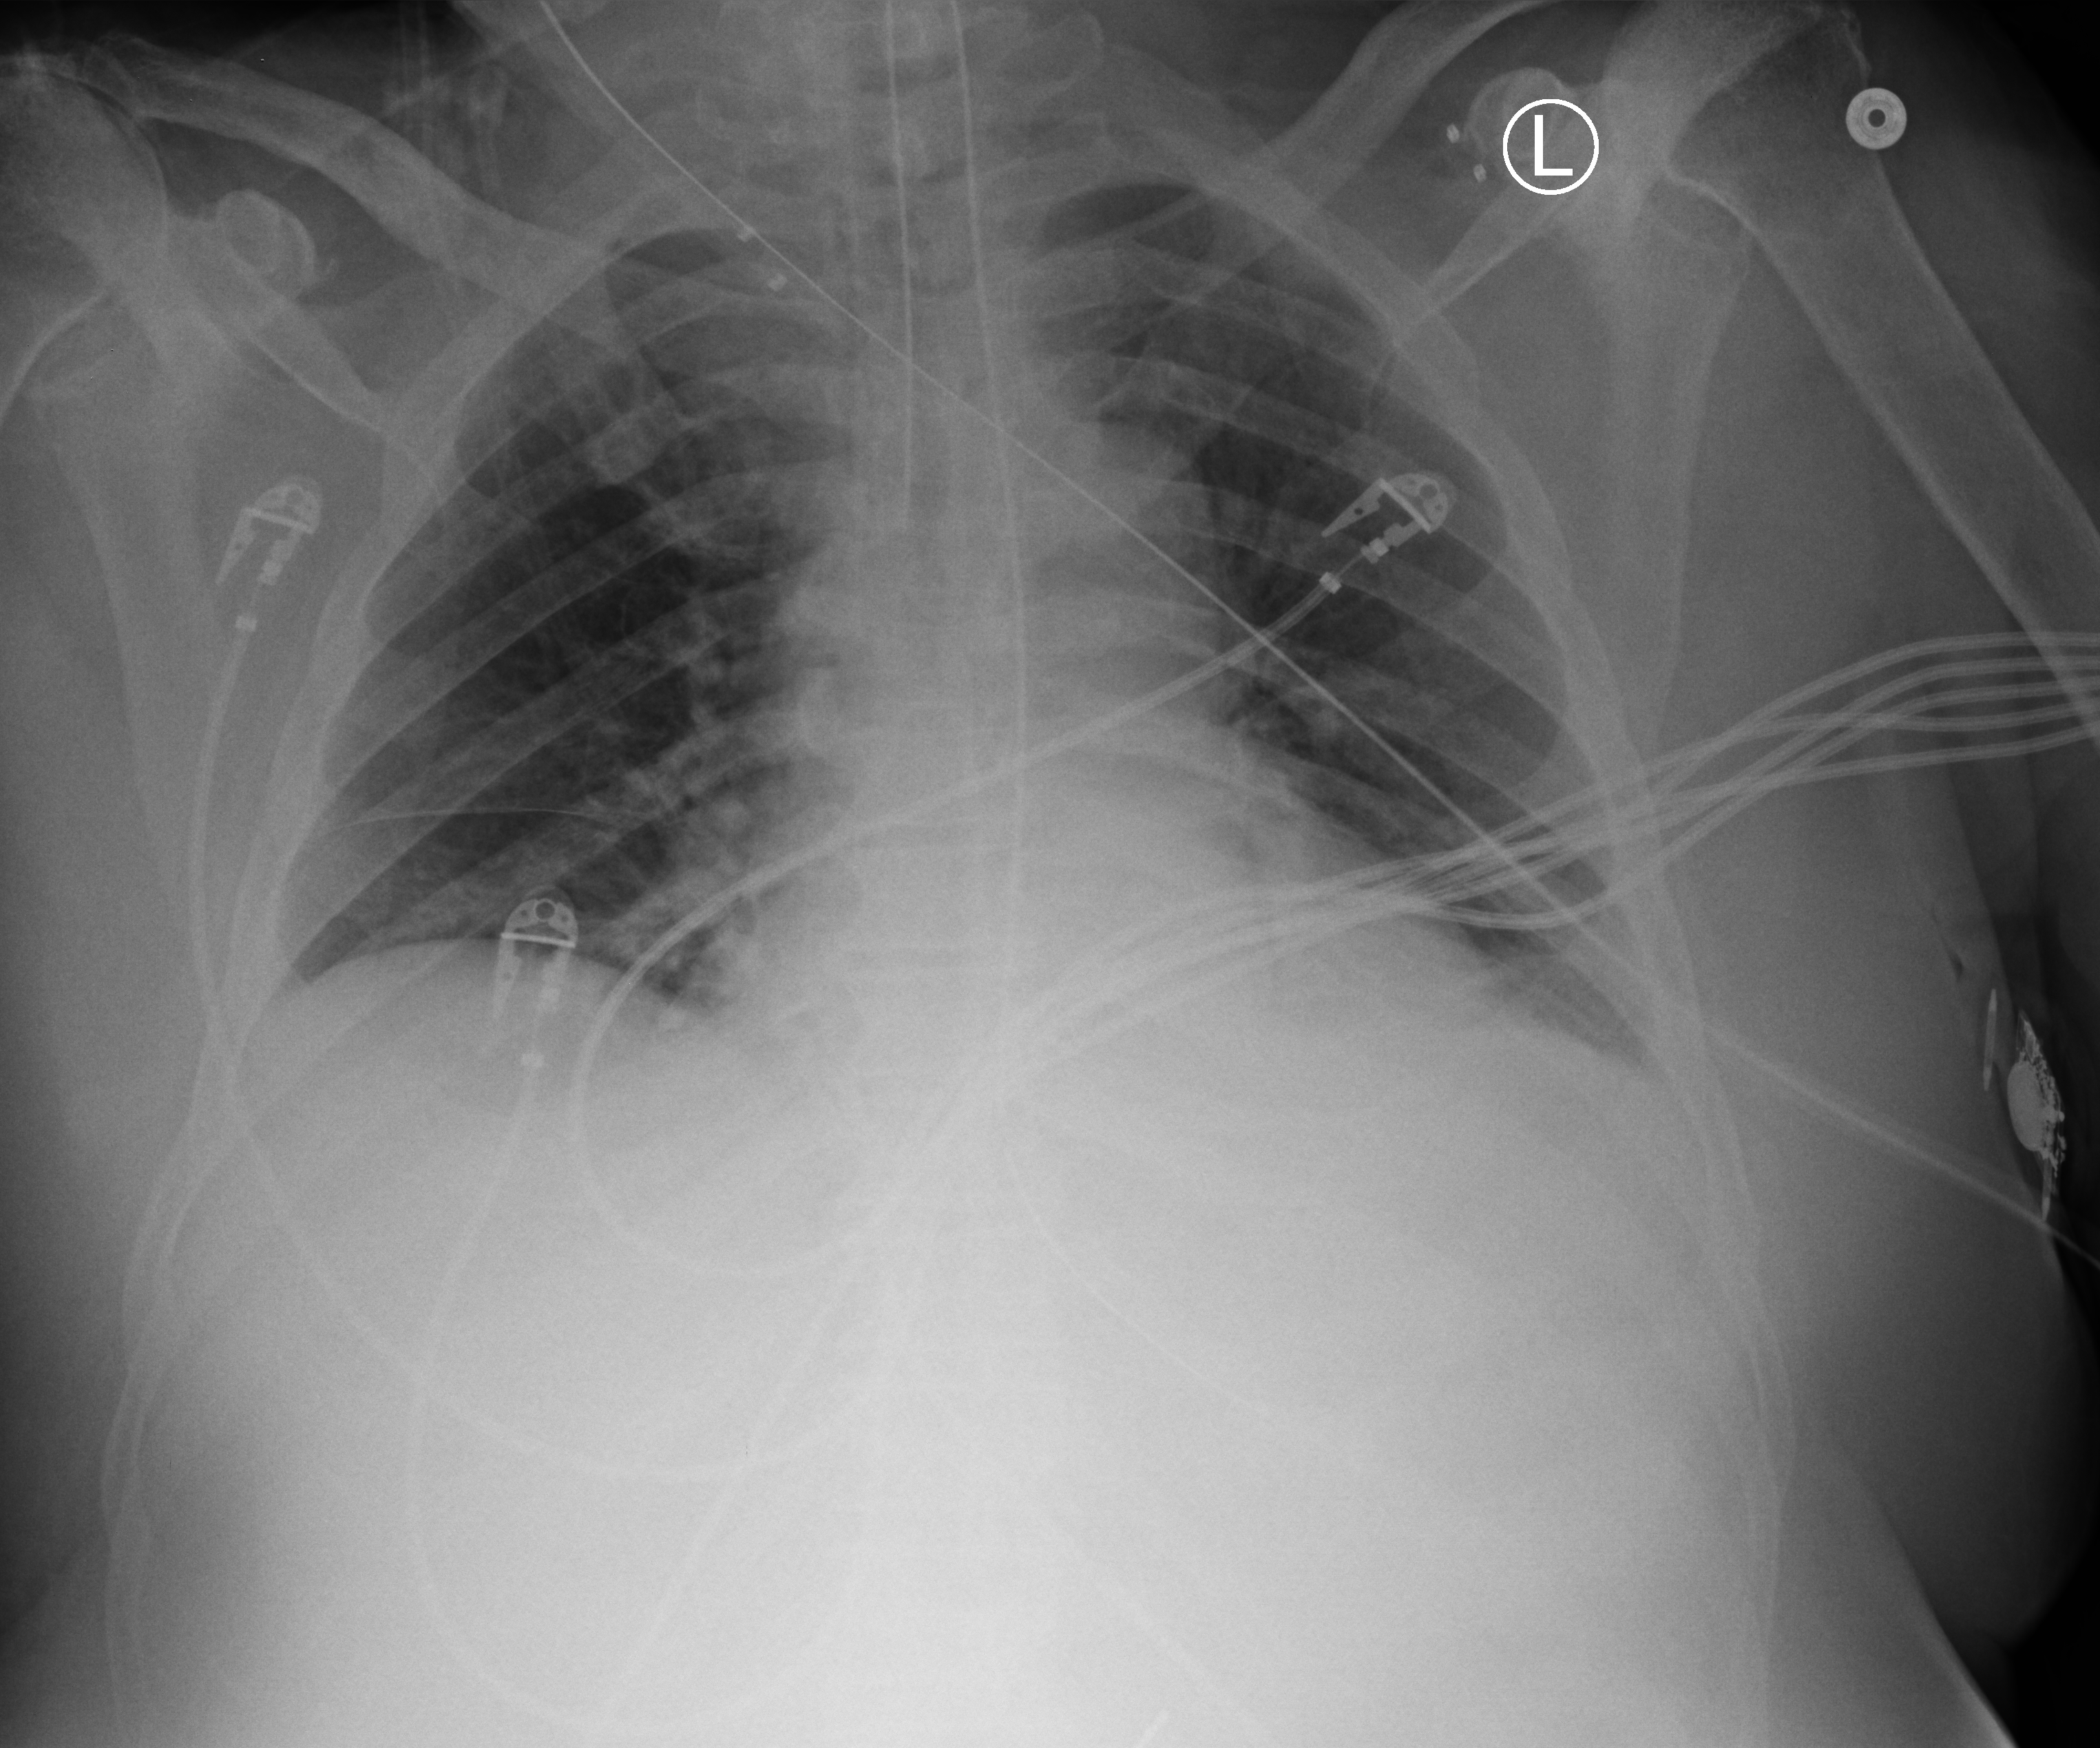
Bedside chest radiograph (computed radiography), anteroposterior (AP) projection. Patient hospitalised with COVID-19; male, aged 75–90 years.
From the hospital-stay record, not from the radiograph (when in the stay this image was taken is not recorded):
- admitted to intensive care during this hospital stay: yes